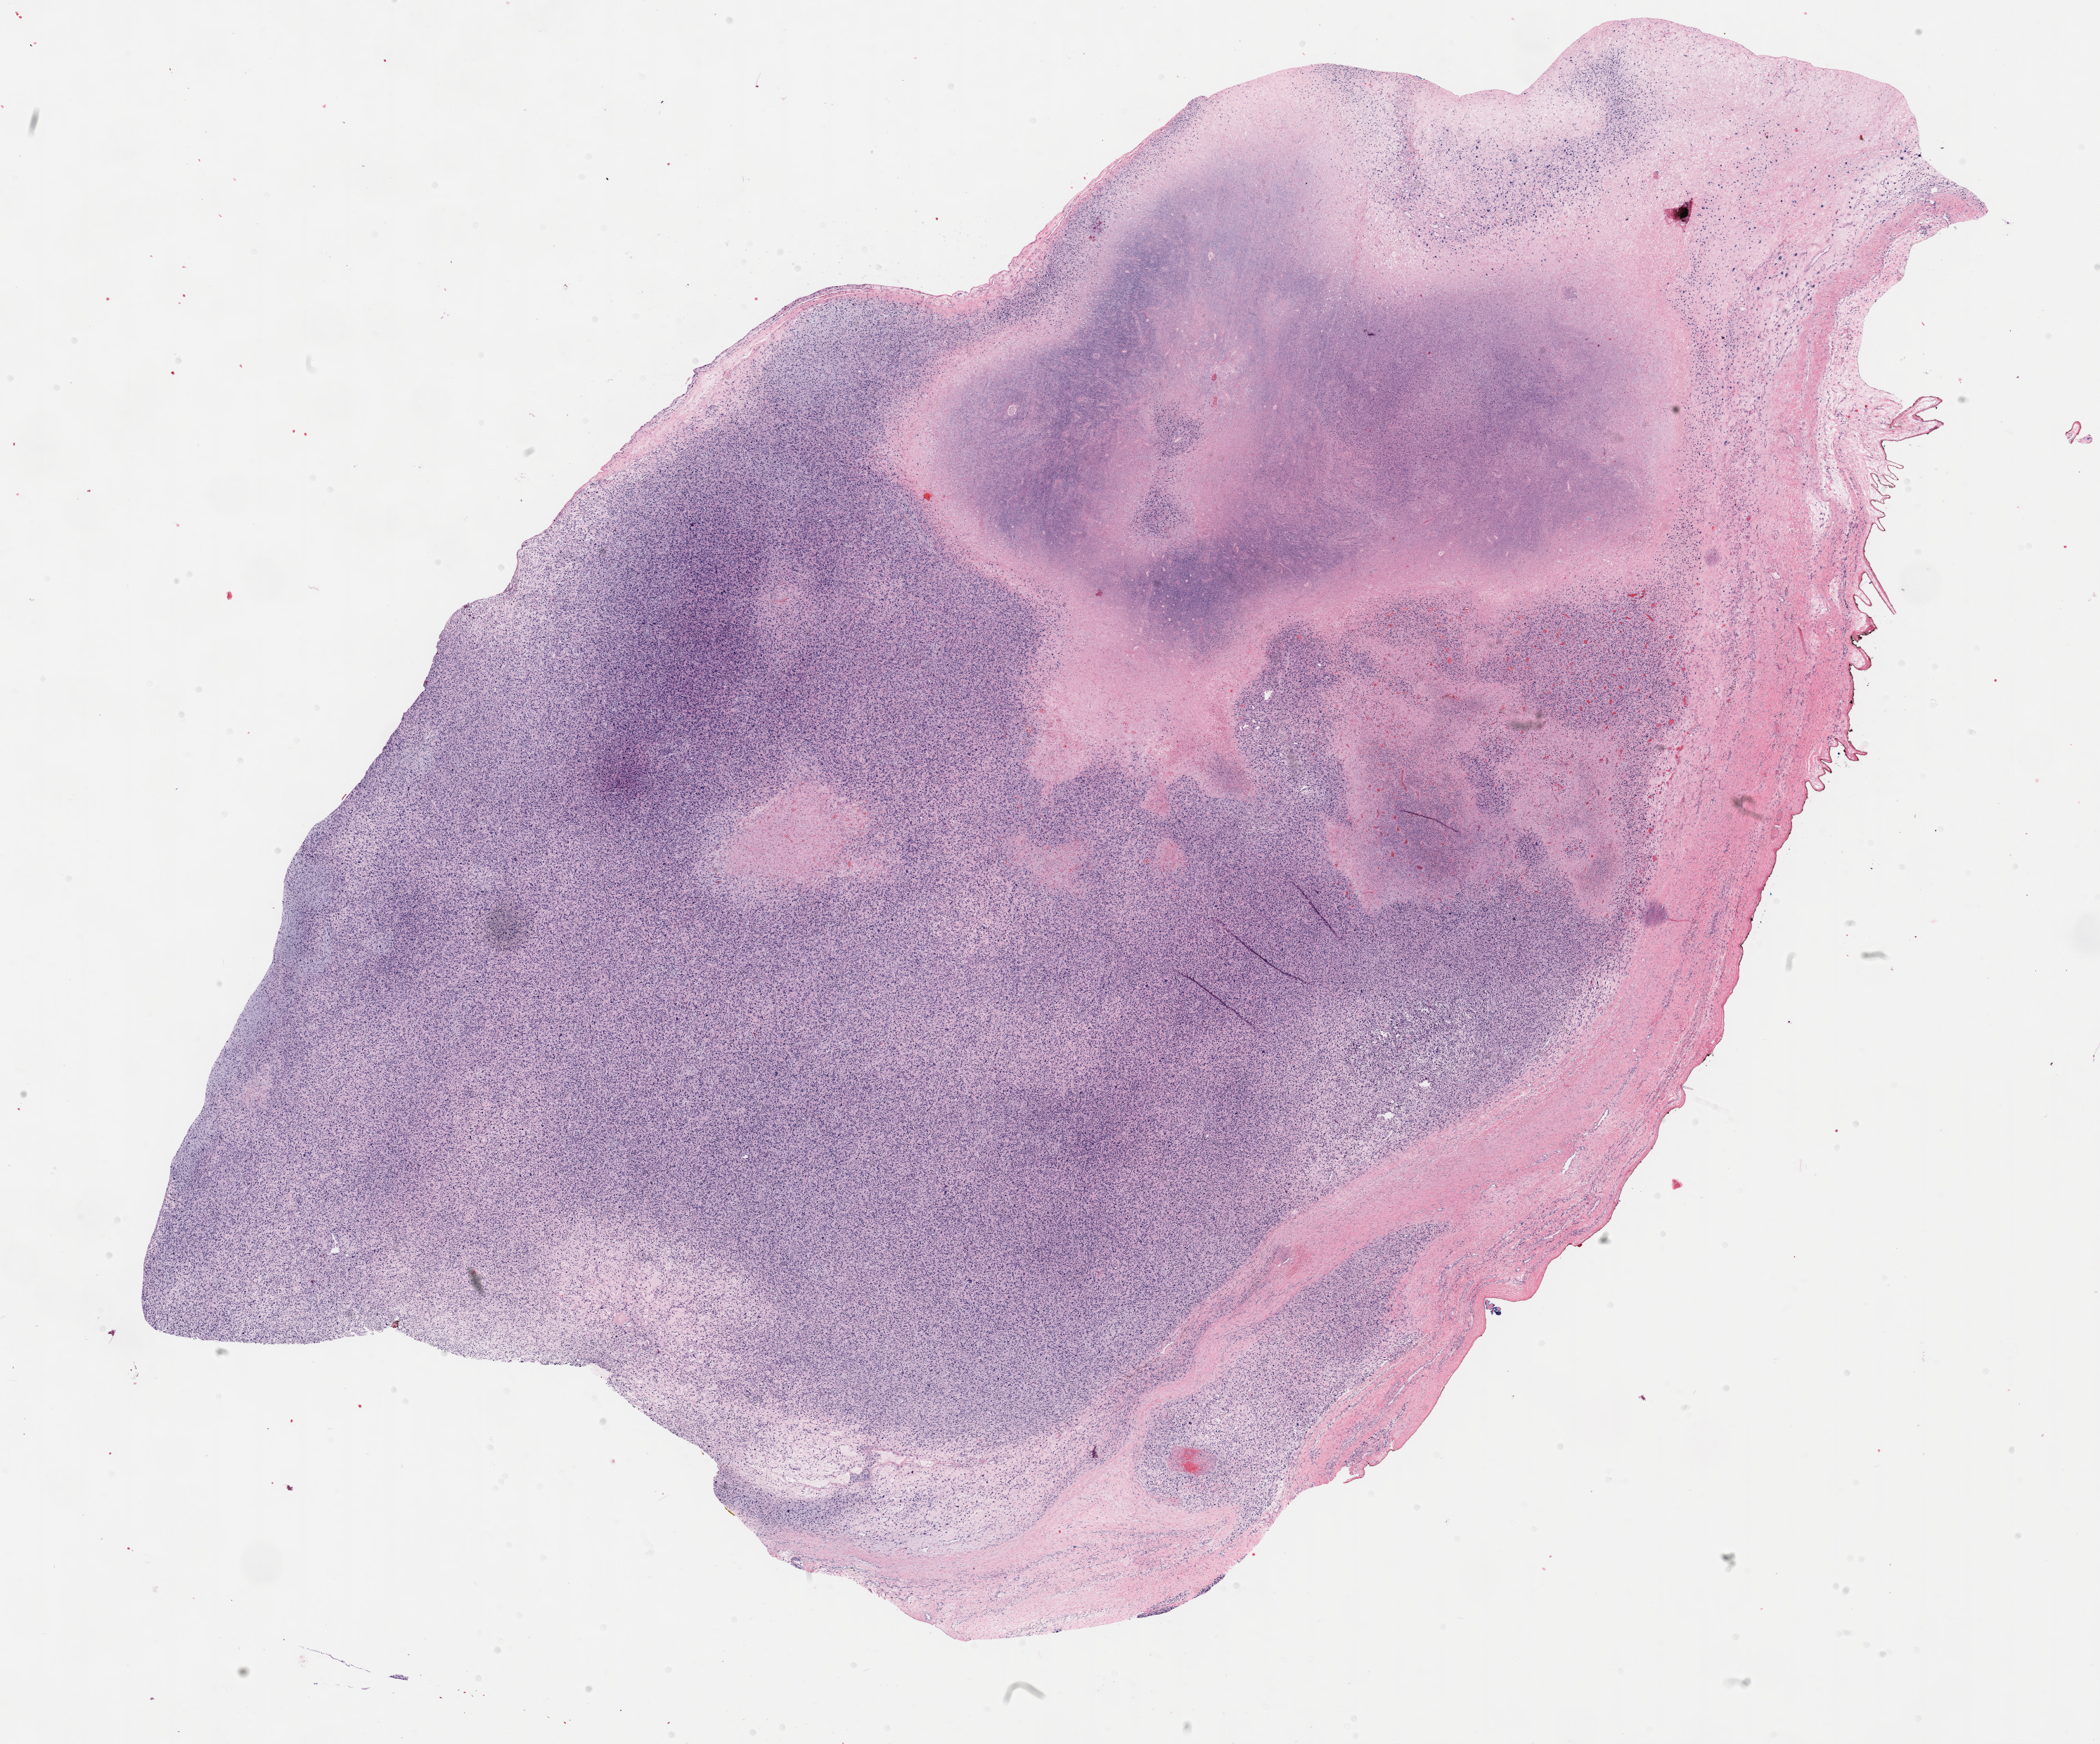
Hematoxylin and eosin (H&E) stained whole-slide image — a low-resolution overview of the entire scanned area, about 24.2 x 20.1 mm (slide scanned at 40x), formalin-fixed paraffin-embedded (FFPE) diagnostic section, sample: primary tumour, connective, subcutaneous and other soft tissues. Female patient; age at initial diagnosis 72 years.
• diagnosis: Undifferentiated sarcoma (connective, subcutaneous and other soft tissues of lower limb and hip)